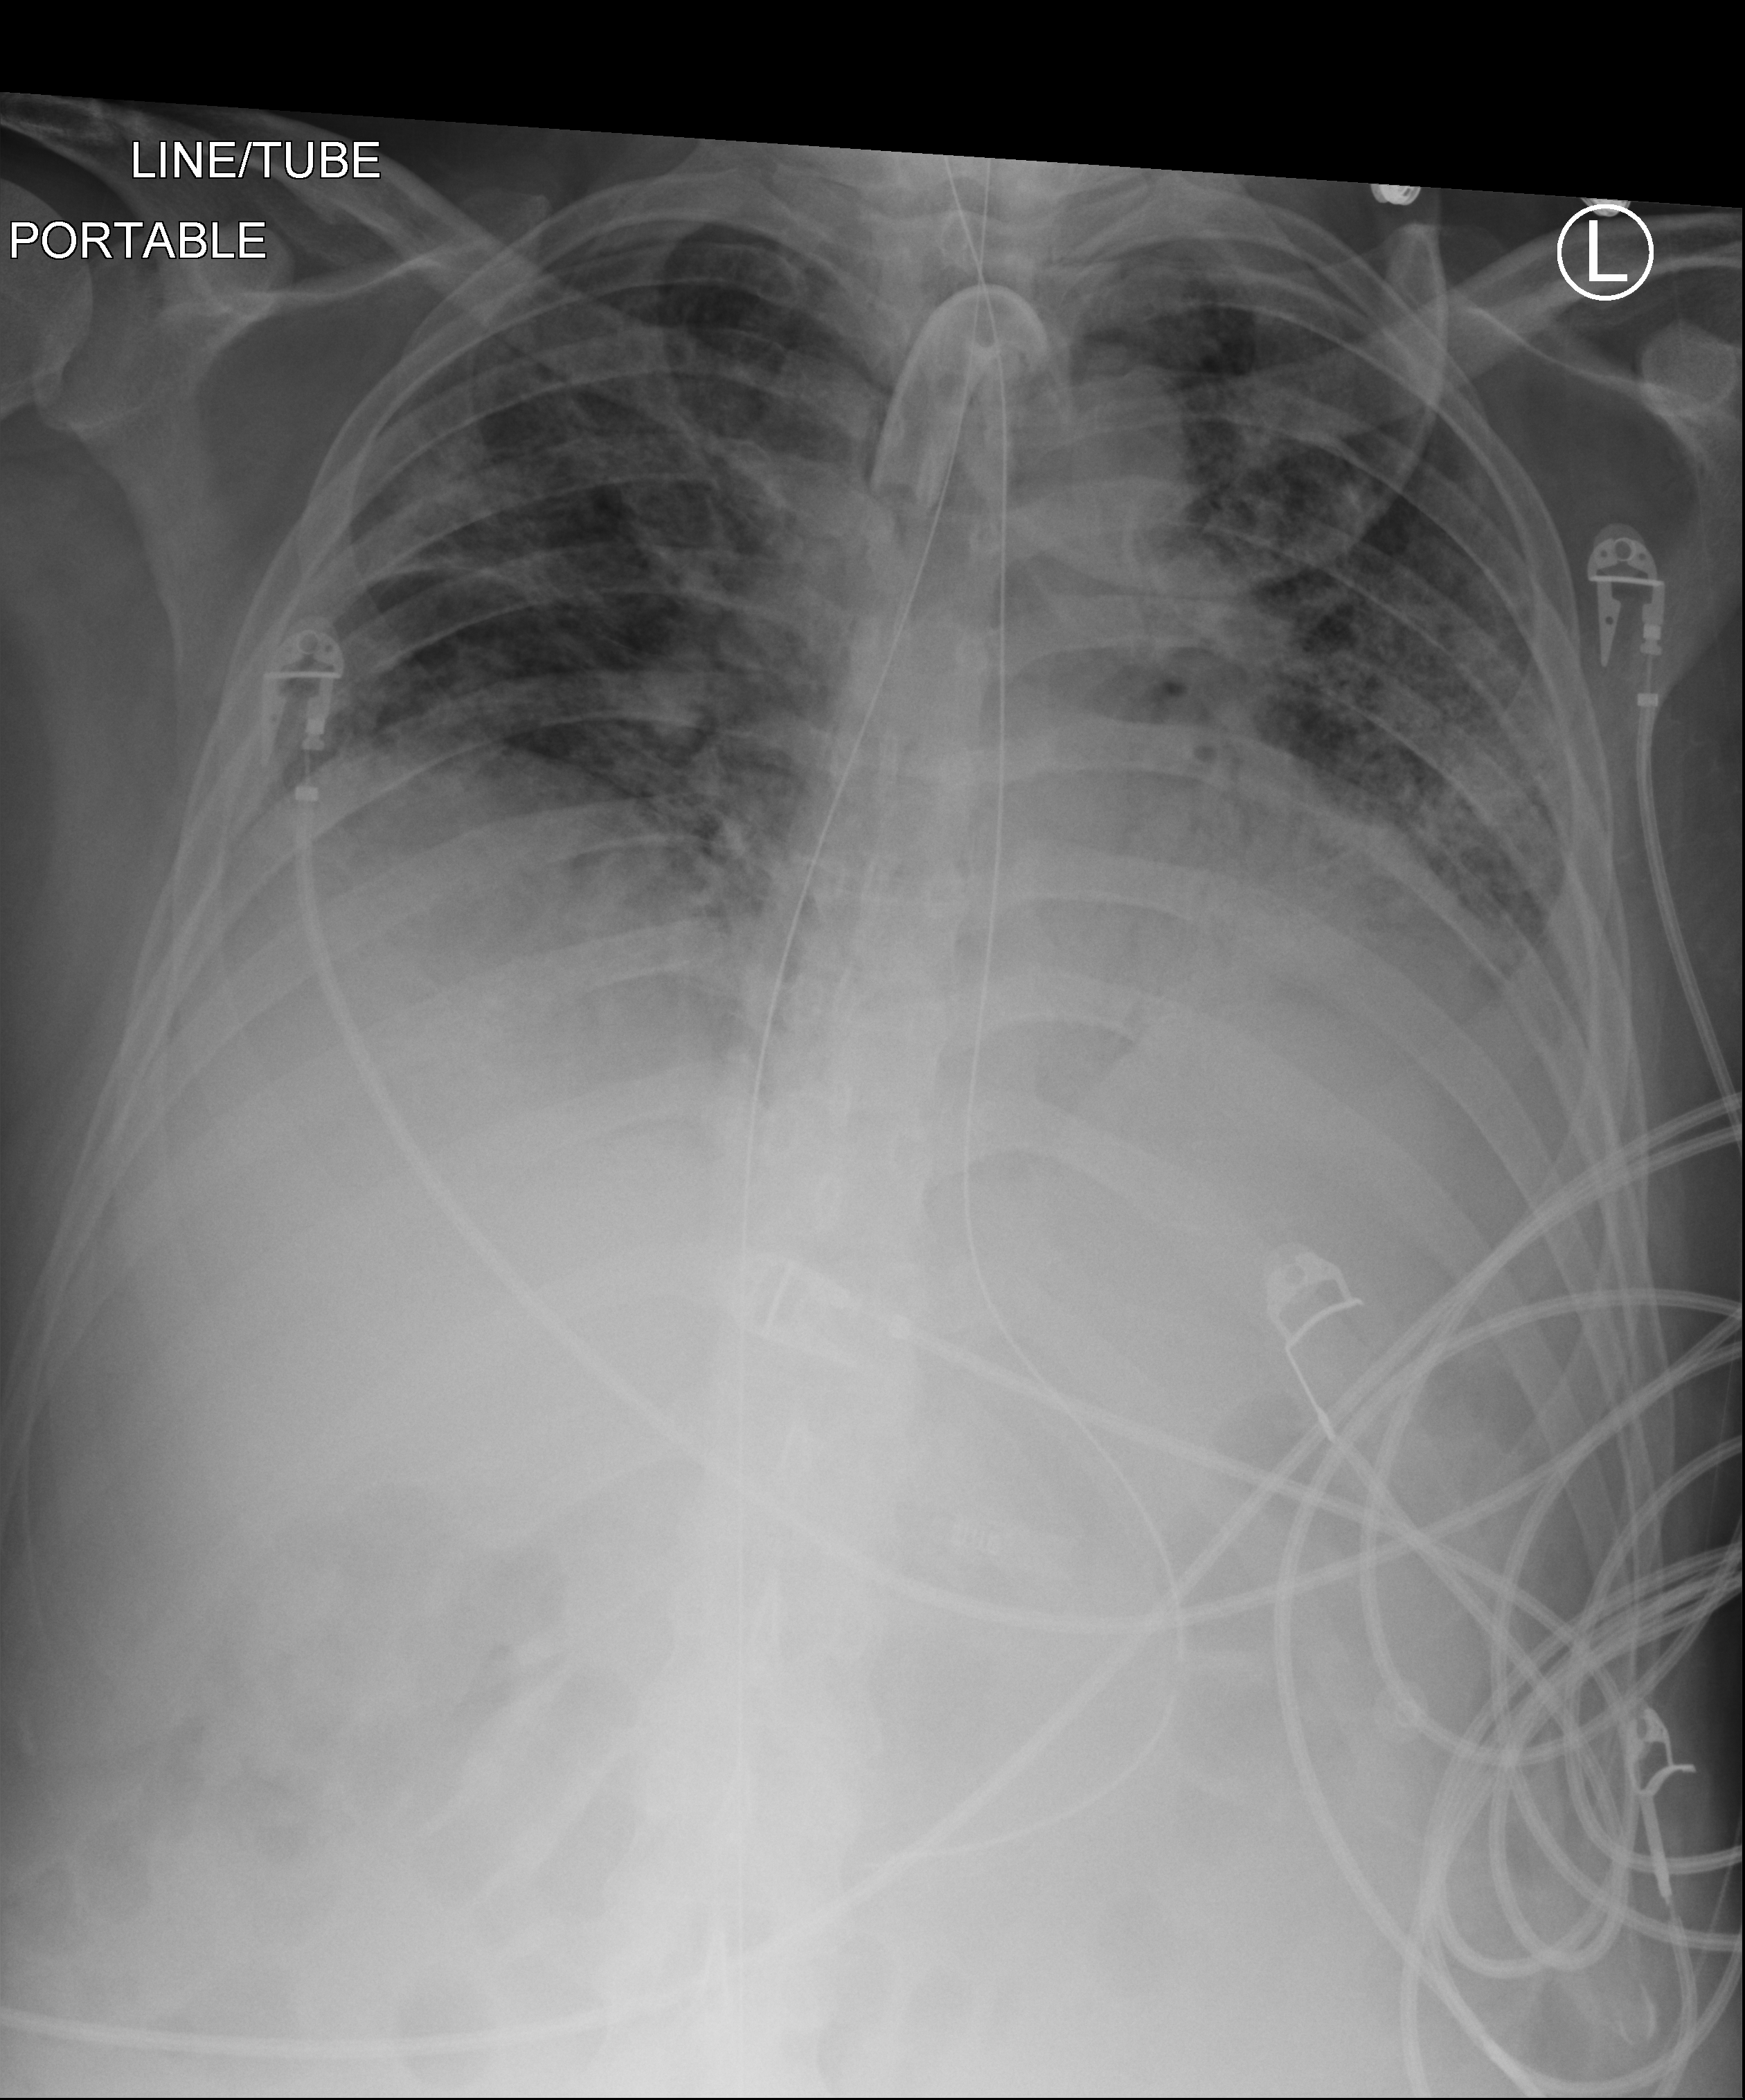
Portable chest radiograph. Male patient hospitalised with COVID-19, age 18–59 years.
Admission-level facts for this patient (not findings on this image; timing relative to this image not recorded): COPD (admission record): no; admitted to intensive care during this hospital stay: yes.